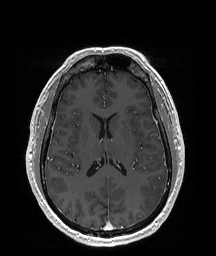
Brain MRI from a brain-tumour surgery series, one axial slice; slice 88 of 192 in the series (ordered by position); T1-weighted post-contrast; 1 mm slice thickness; 216 × 256 image matrix, field of view 219 × 260 mm. From the clinical record (not read from this slice): histopathology: Glioblastoma; WHO grade: 4; IDH mutation: no.
Structures marked on this image (outlined manually by an expert reader):
- tumour: box from (x=140, y=177) to (x=167, y=211) px